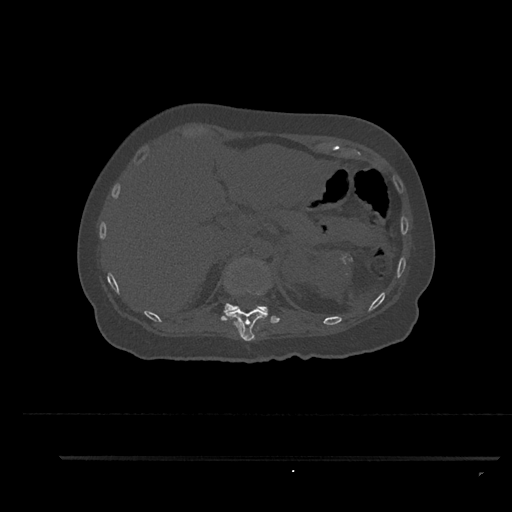
CT including the spine, one axial slice; slice 294 of 797 in the series (ordered by position); reconstruction kernel Br40s/3; 120 kVp; bone window (W 1800 / L 400 HU); 0.5 mm slice thickness; 512 × 512 image matrix, field of view 408 × 408 mm. Female patient, age 44 years. Case-level facts recorded for this patient, not image findings: primary cancer: renal.
Structures marked on this image (semi-automatically segmented with operator editing):
- T11 vertebra: bounding box <230,264,271,341> (left, top, right, bottom; pixels)
- T12 vertebra: <220,259,279,321>